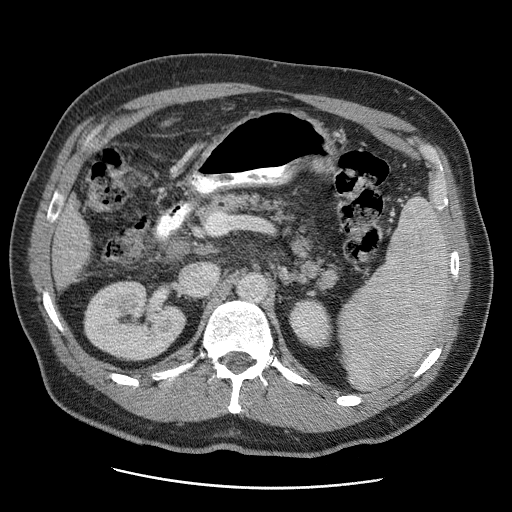
Contrast-enhanced abdominal CT (liver protocol), one axial slice. Slice 14 of 81 in the series (ordered by position). Soft-tissue window (W 400 / L 40 HU). 2.5 mm slice thickness. 512 × 512 image matrix, field of view 380 × 380 mm. Case-level facts recorded for this patient, not image findings: diagnosis: hepatocellular carcinoma (patient treated with transarterial chemoembolisation; whether this scan precedes or follows treatment is not stated here); TNM stage (as recorded): Stage-IIIA; Child-Pugh class: A; tumour differentiation: moderately differentiated.
Structures marked on this image (semi-automatic segmentation, software-assisted and operator-edited):
- liver parenchyma outside the tumour (the mass and vessels are separate outlines, so this box may not span the whole liver): bounding box <52,195,90,288> (left, top, right, bottom; pixels)